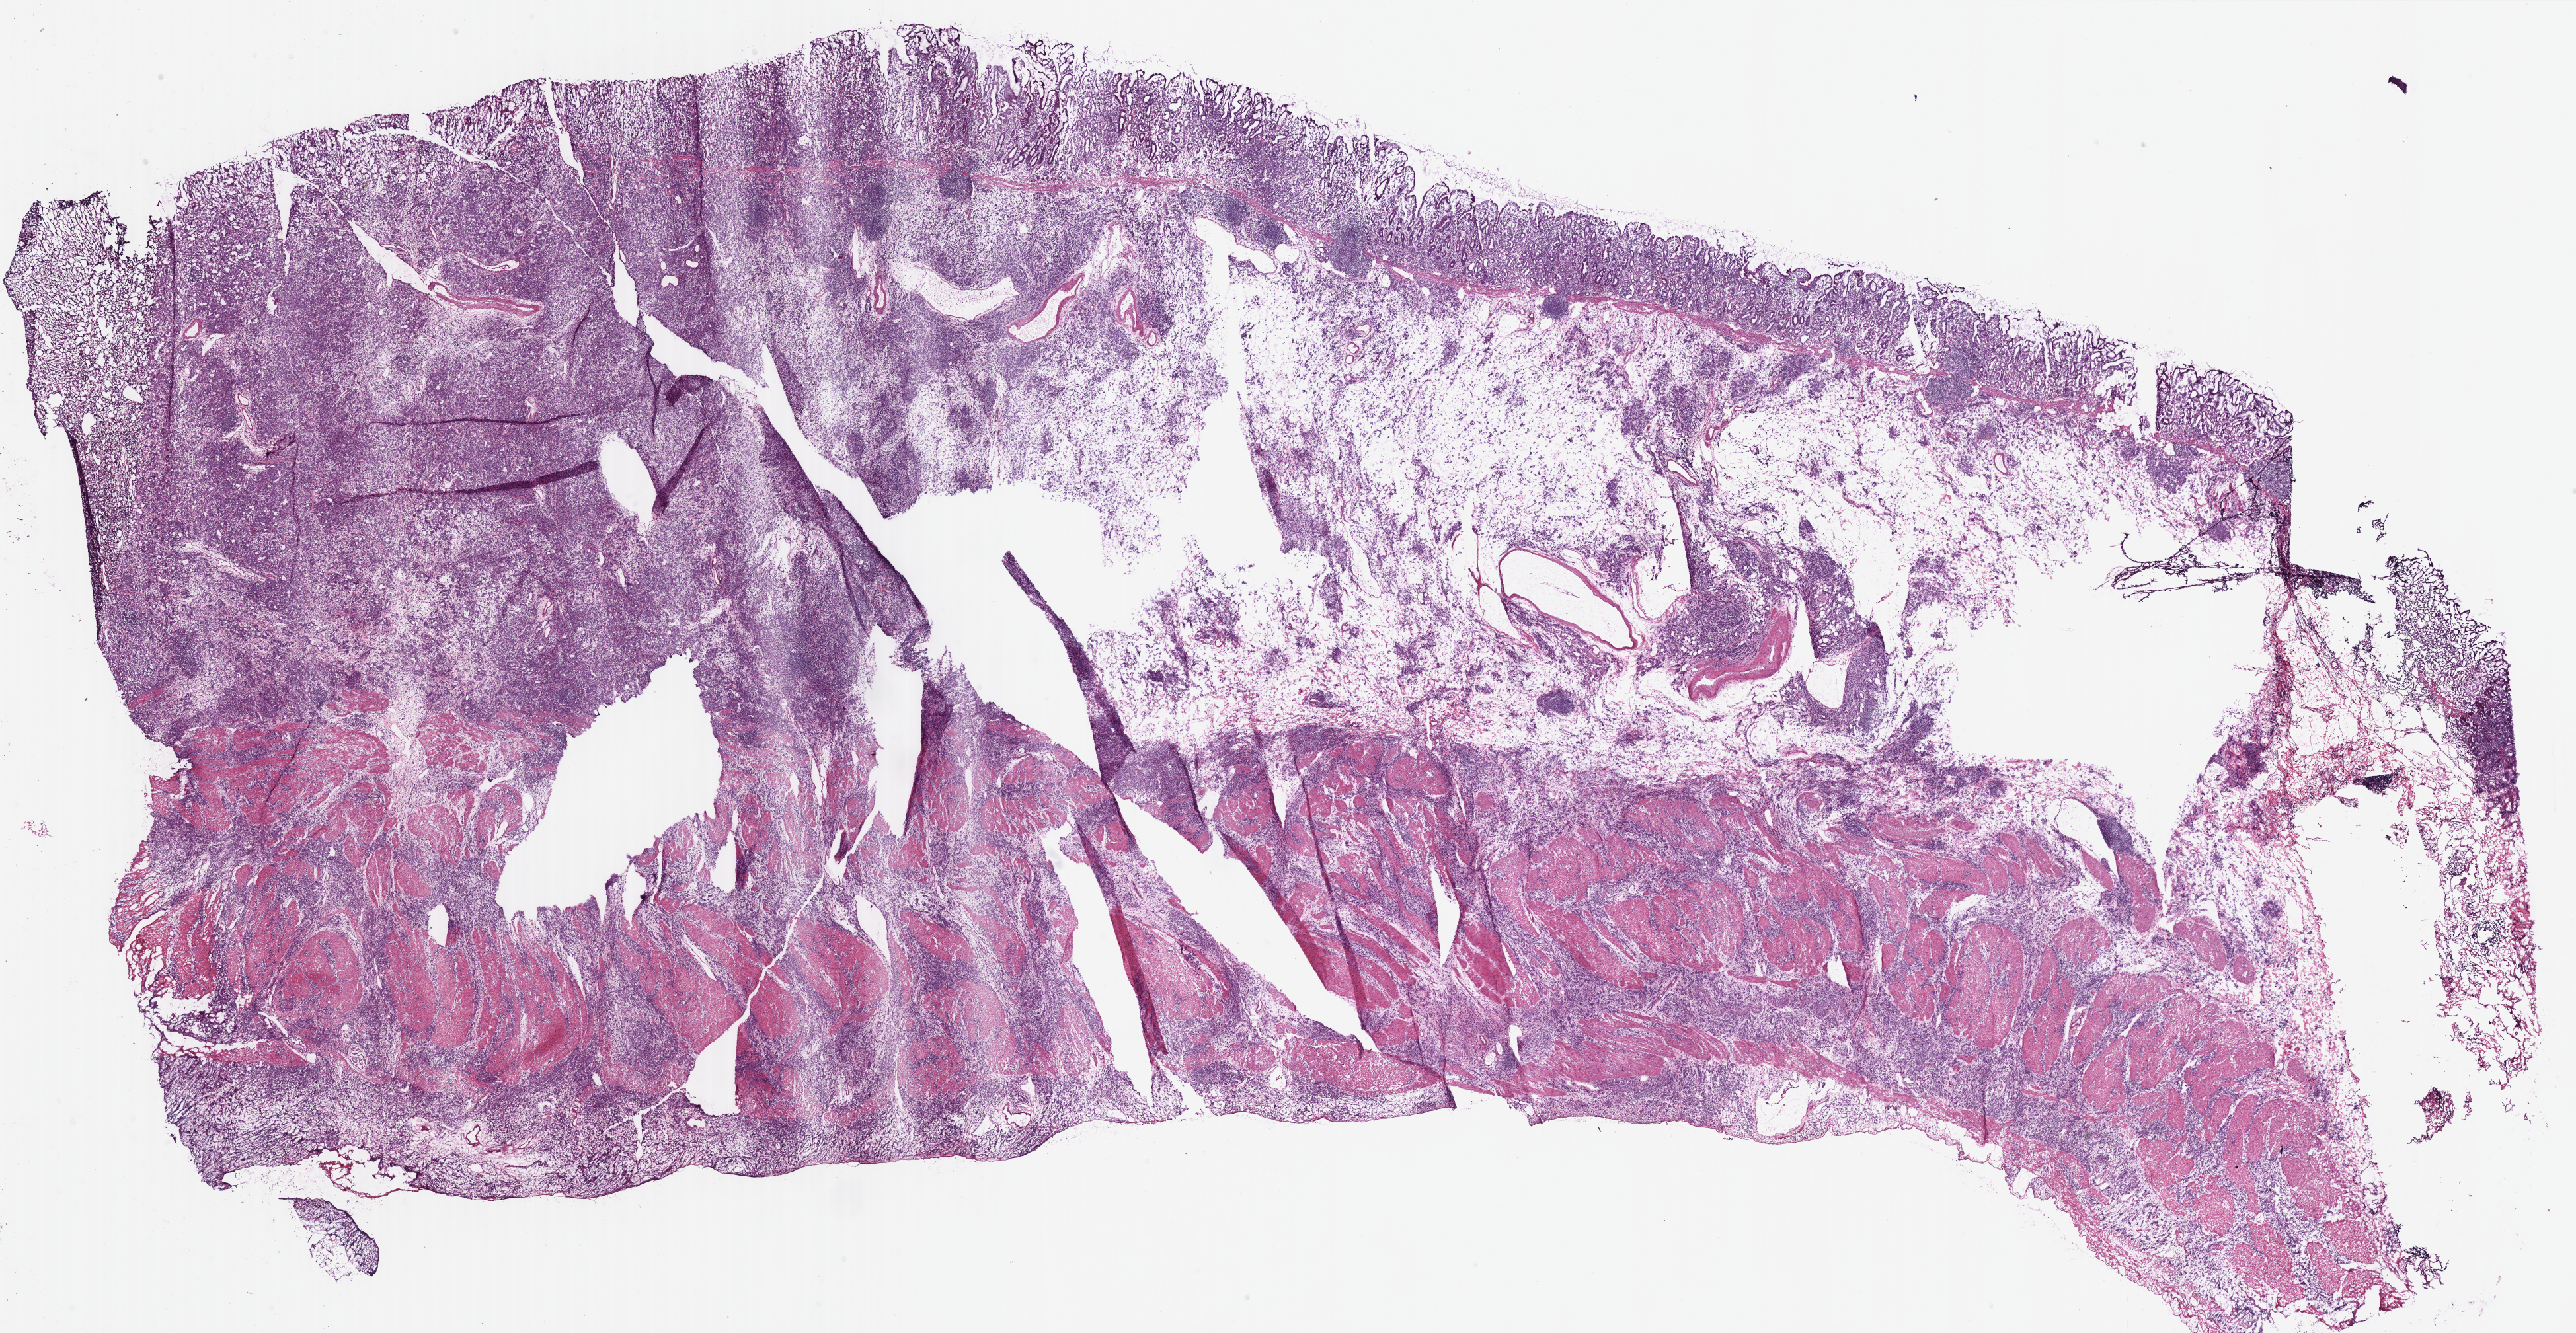
H&E-stained whole-slide image — whole scanned area (about 30.7 x 15.9 mm) shown as a low-resolution overview, frozen section, sample: primary tumour, stomach. Patient: male, age at initial diagnosis 69 years. Histologic grade: G3 (poorly differentiated). Pathologist review of this section (percent, as recorded): tumour cells 90%, tumour nuclei 80%, normal cells 10%, stromal cells 0%, necrosis 0%. Inflammatory infiltration, as recorded: lymphocyte infiltration 5%, monocyte infiltration 0%, neutrophil infiltration 5%.
• pathologic diagnosis: Tubular adenocarcinoma (gastric antrum)
• AJCC pathologic stage: IIIB (7th edition)